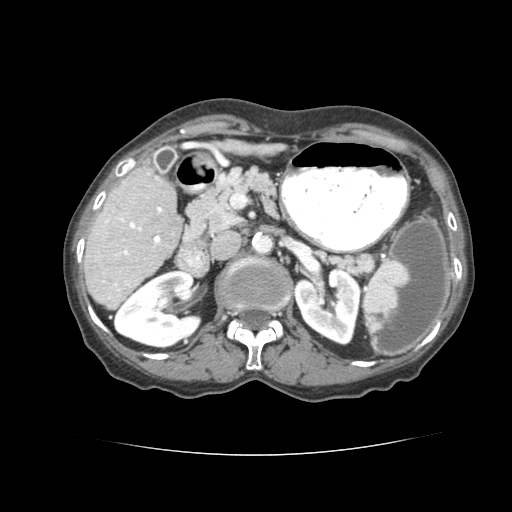
Contrast-enhanced abdominal CT (liver protocol), one axial slice; slice 32 of 77 in the series (ordered by position); reconstruction kernel STANDARD; 120 kVp; soft-tissue window (W 400 / L 40 HU); 2.5 mm slice thickness; 512 × 512 image matrix, field of view 340 × 340 mm. Case-level facts recorded for this patient, not image findings: diagnosis: hepatocellular carcinoma (patient treated with transarterial chemoembolisation; whether this scan precedes or follows treatment is not stated here); TNM stage (as recorded): Stage-I; Child-Pugh class: A; tumour differentiation: well differentiated; tumour nodularity: uninodular.
Outlined on this slice (semi-automatic segmentation, software-assisted and operator-edited):
- liver parenchyma outside the tumour (the mass and vessels are separate outlines, so this box may not span the whole liver): bounding box <82,157,182,306> (left, top, right, bottom; pixels)
- liver vessels: <125,167,161,239>